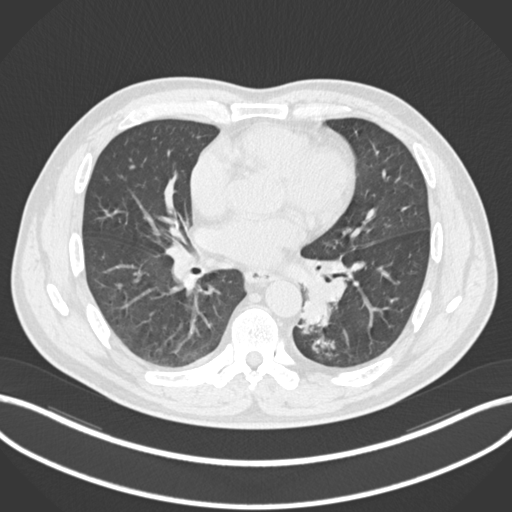
Chest CT, one axial slice. Slice 106 of 223 in the series (ordered by position). Reconstruction kernel B30f. 120 kVp. Lung window (W 1500 / L -600 HU). 512 × 512 image matrix, field of view 400 × 400 mm. Patient: male, 50 years. From the clinical record (not read from this slice): clinical TNM (as recorded): T2a N3 M0.
Outlined on this slice (rectangle marked by the reading radiologist):
- lung tumour (recorded histology: squamous cell carcinoma): bounding box (x1, y1, x2, y2) in pixels: (297, 272, 346, 330)